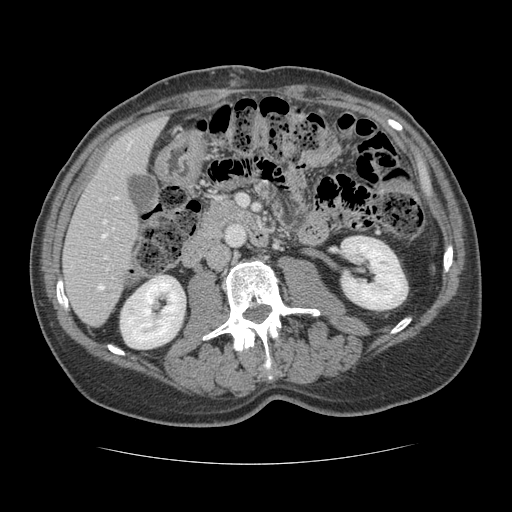
Contrast-enhanced abdominal CT, one axial slice; slice 49 of 134 in the series (ordered by position); reconstruction kernel STANDARD; 120 kVp; intravenous contrast given; soft-tissue window (W 400 / L 40 HU); 2.5 mm slice thickness; 512 × 512 image matrix, field of view 377 × 377 mm. Male patient, age 68 years. From the clinical record (not read from this slice): diagnosis: colorectal cancer liver metastases, imaged before liver resection.
Outlined on this slice (outlined manually by an expert reader):
- hepatic veins: bounding box [x1, y1, x2, y2] px = [102, 148, 128, 237]
- liver: [64, 117, 165, 326]
- planned liver remnant (the part of the liver to remain after resection): [64, 118, 164, 326]
- portal vein (with intrahepatic branches): [98, 256, 108, 289]